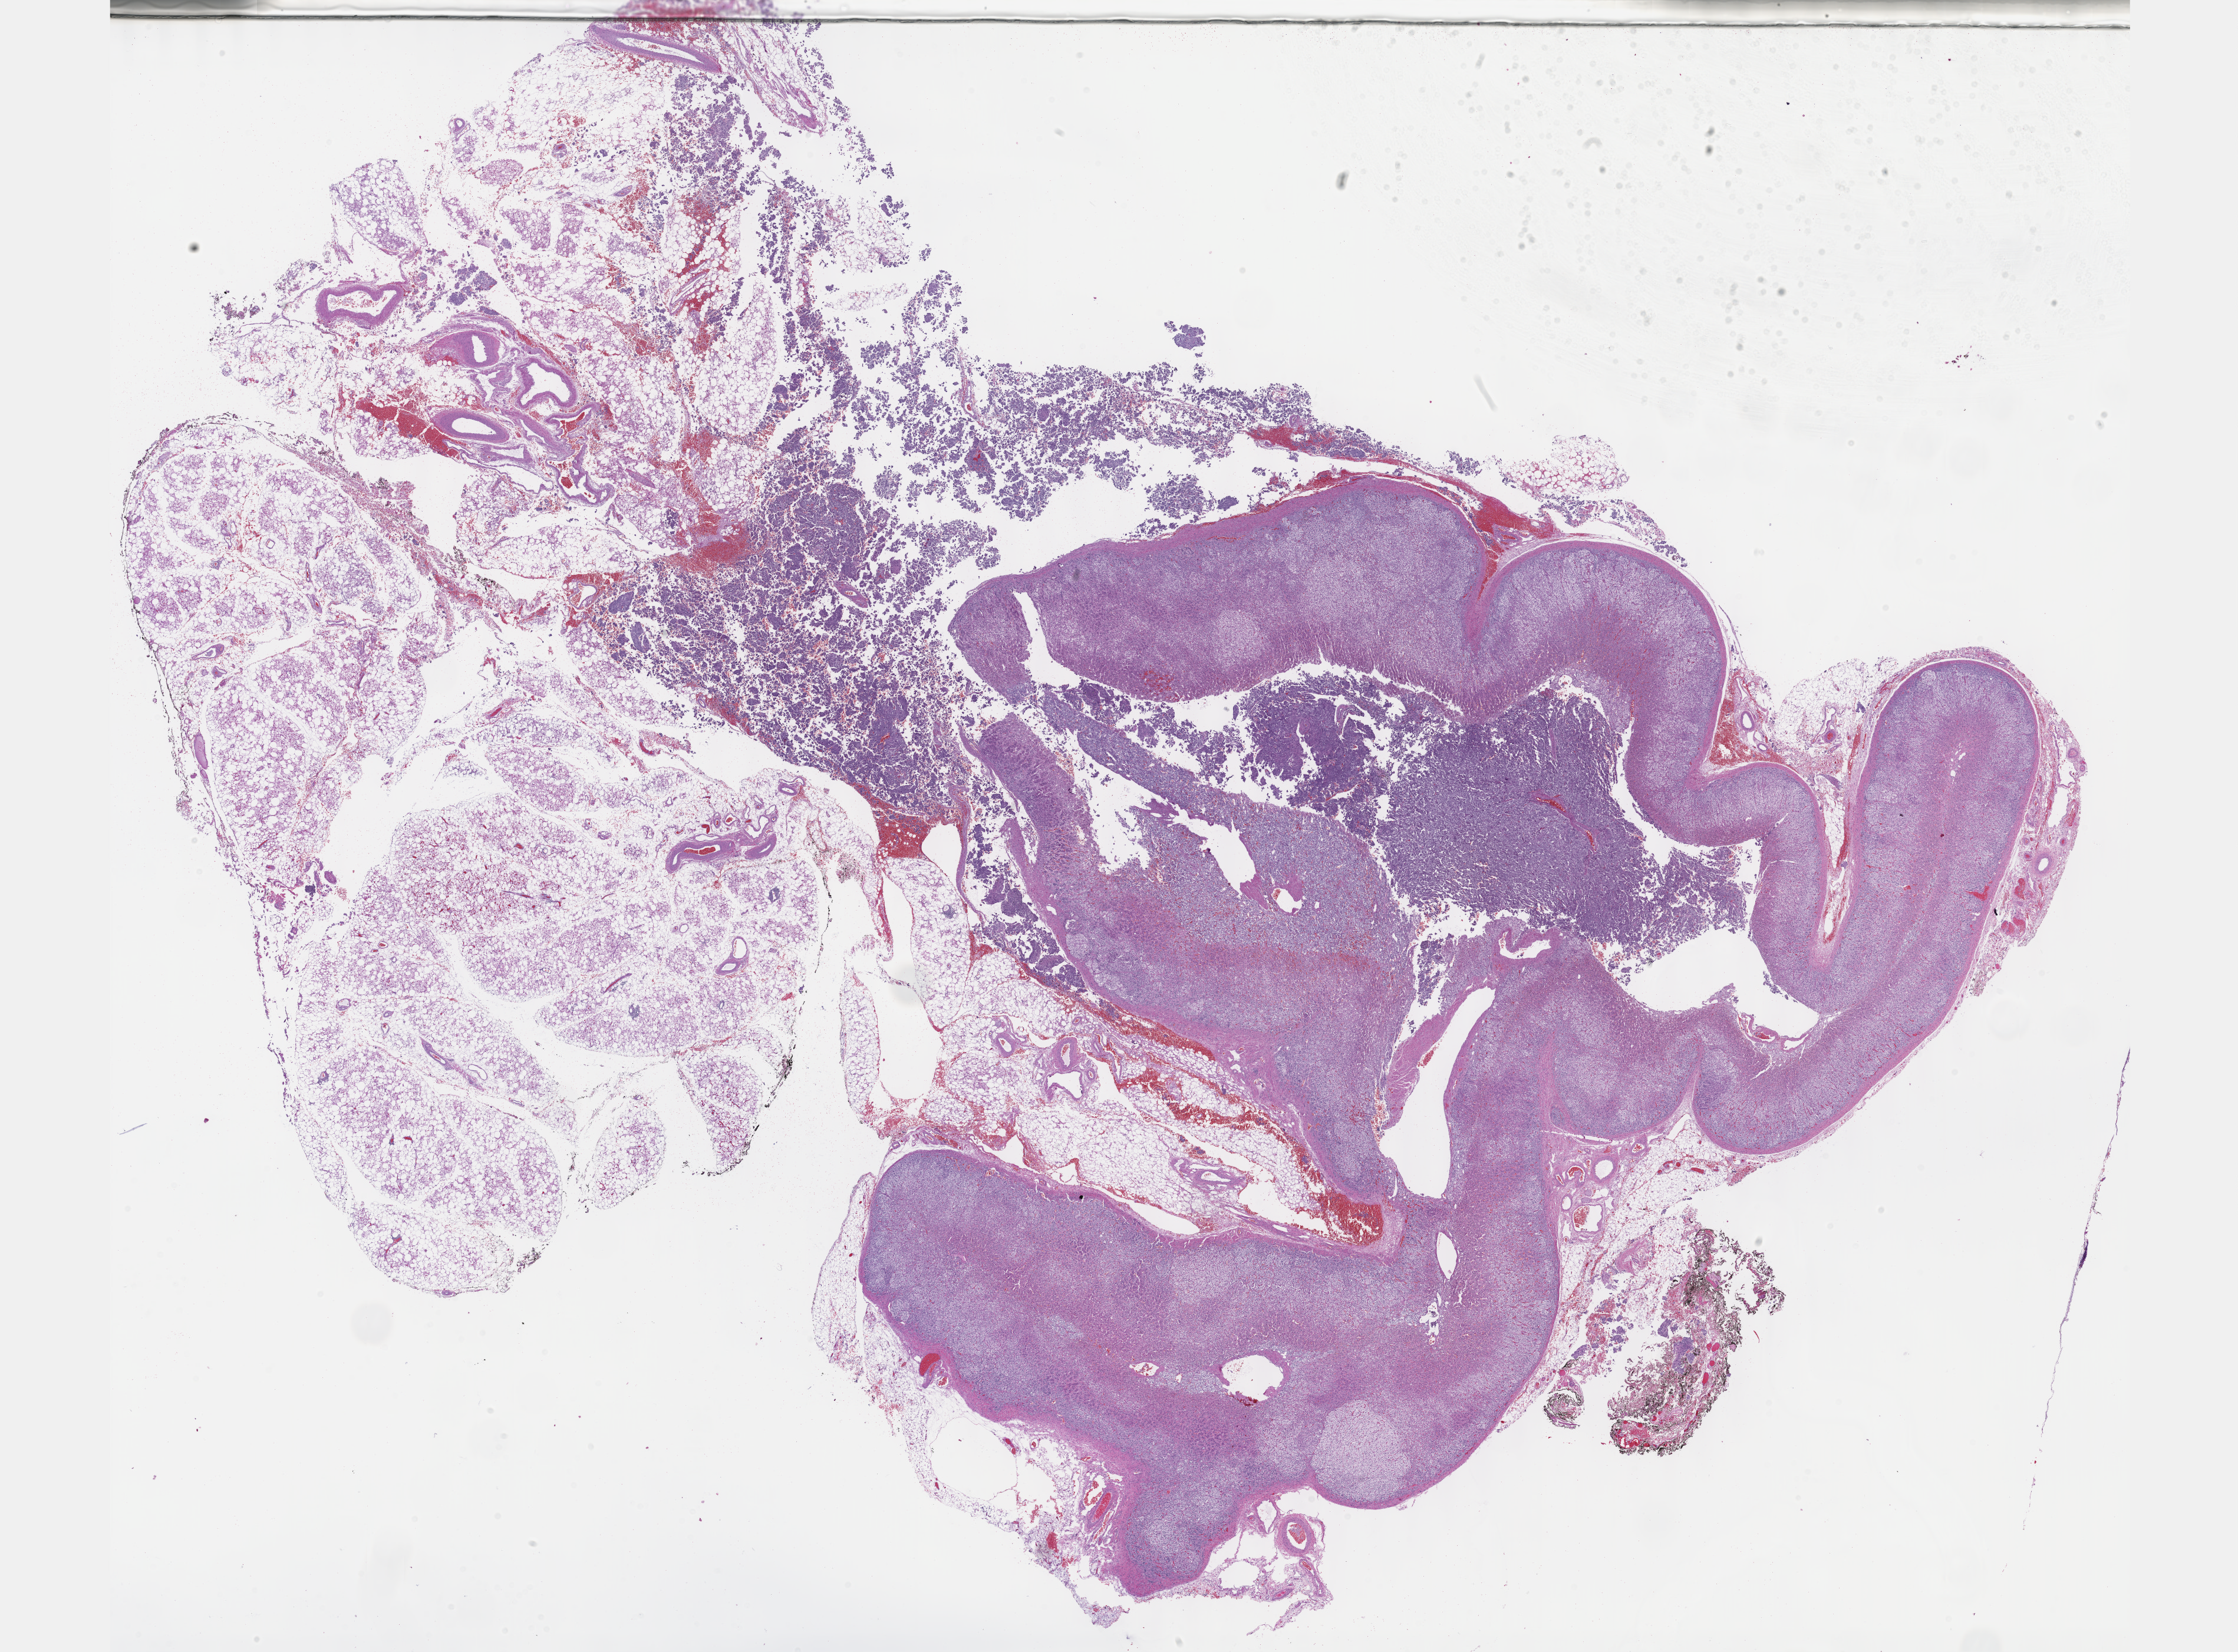
Whole-slide histology image, H&E — shown as a low-resolution overview of the whole scanned area (about 30.7 x 22.6 mm, acquisition: 40x scan), FFPE section, primary tumour sample from the adrenal gland. Male, age 38 years at initial diagnosis.
Diagnosis: Pheochromocytoma, NOS.